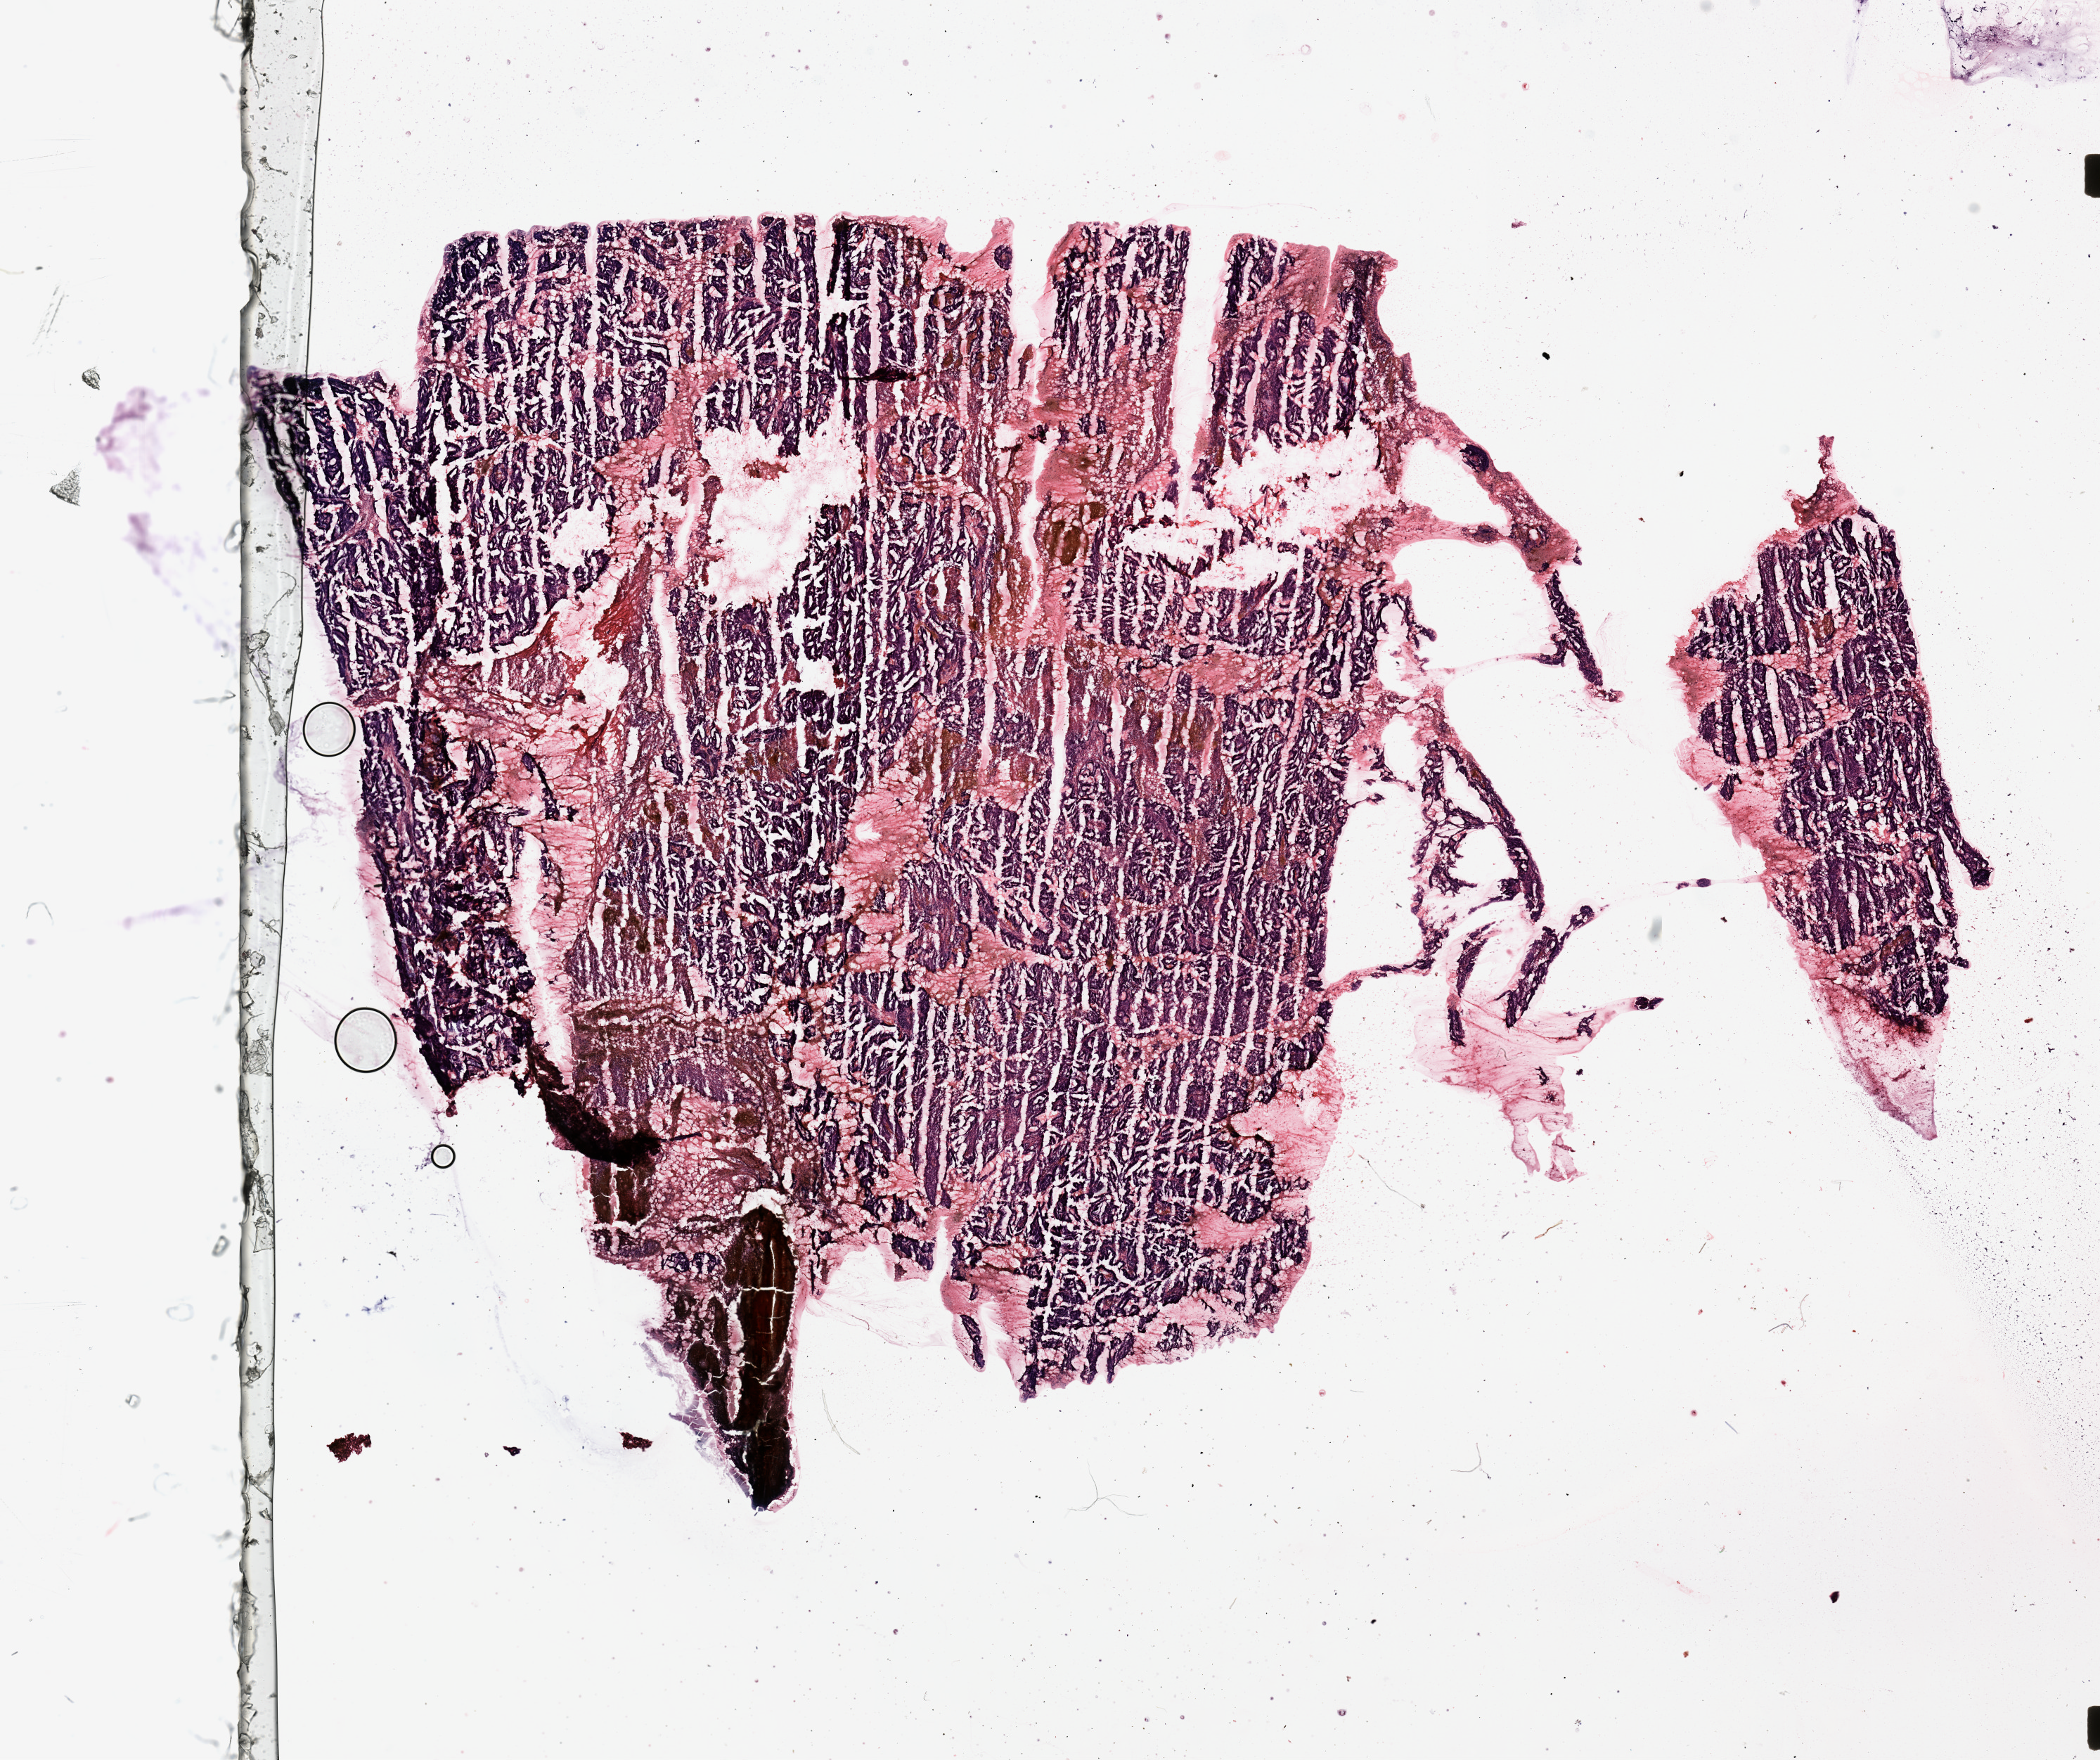
Hematoxylin and eosin (H&E) stained whole-slide image, low-resolution overview of the scanned area, about 23.6 x 19.8 mm (slide scanned at 20x), uterus, tumour tissue. Female, 64 y/o. Histologic grade: G2 (moderately differentiated).
Histologic diagnosis: Endometrioid adenocarcinoma, NOS. AJCC pathologic stage: I.